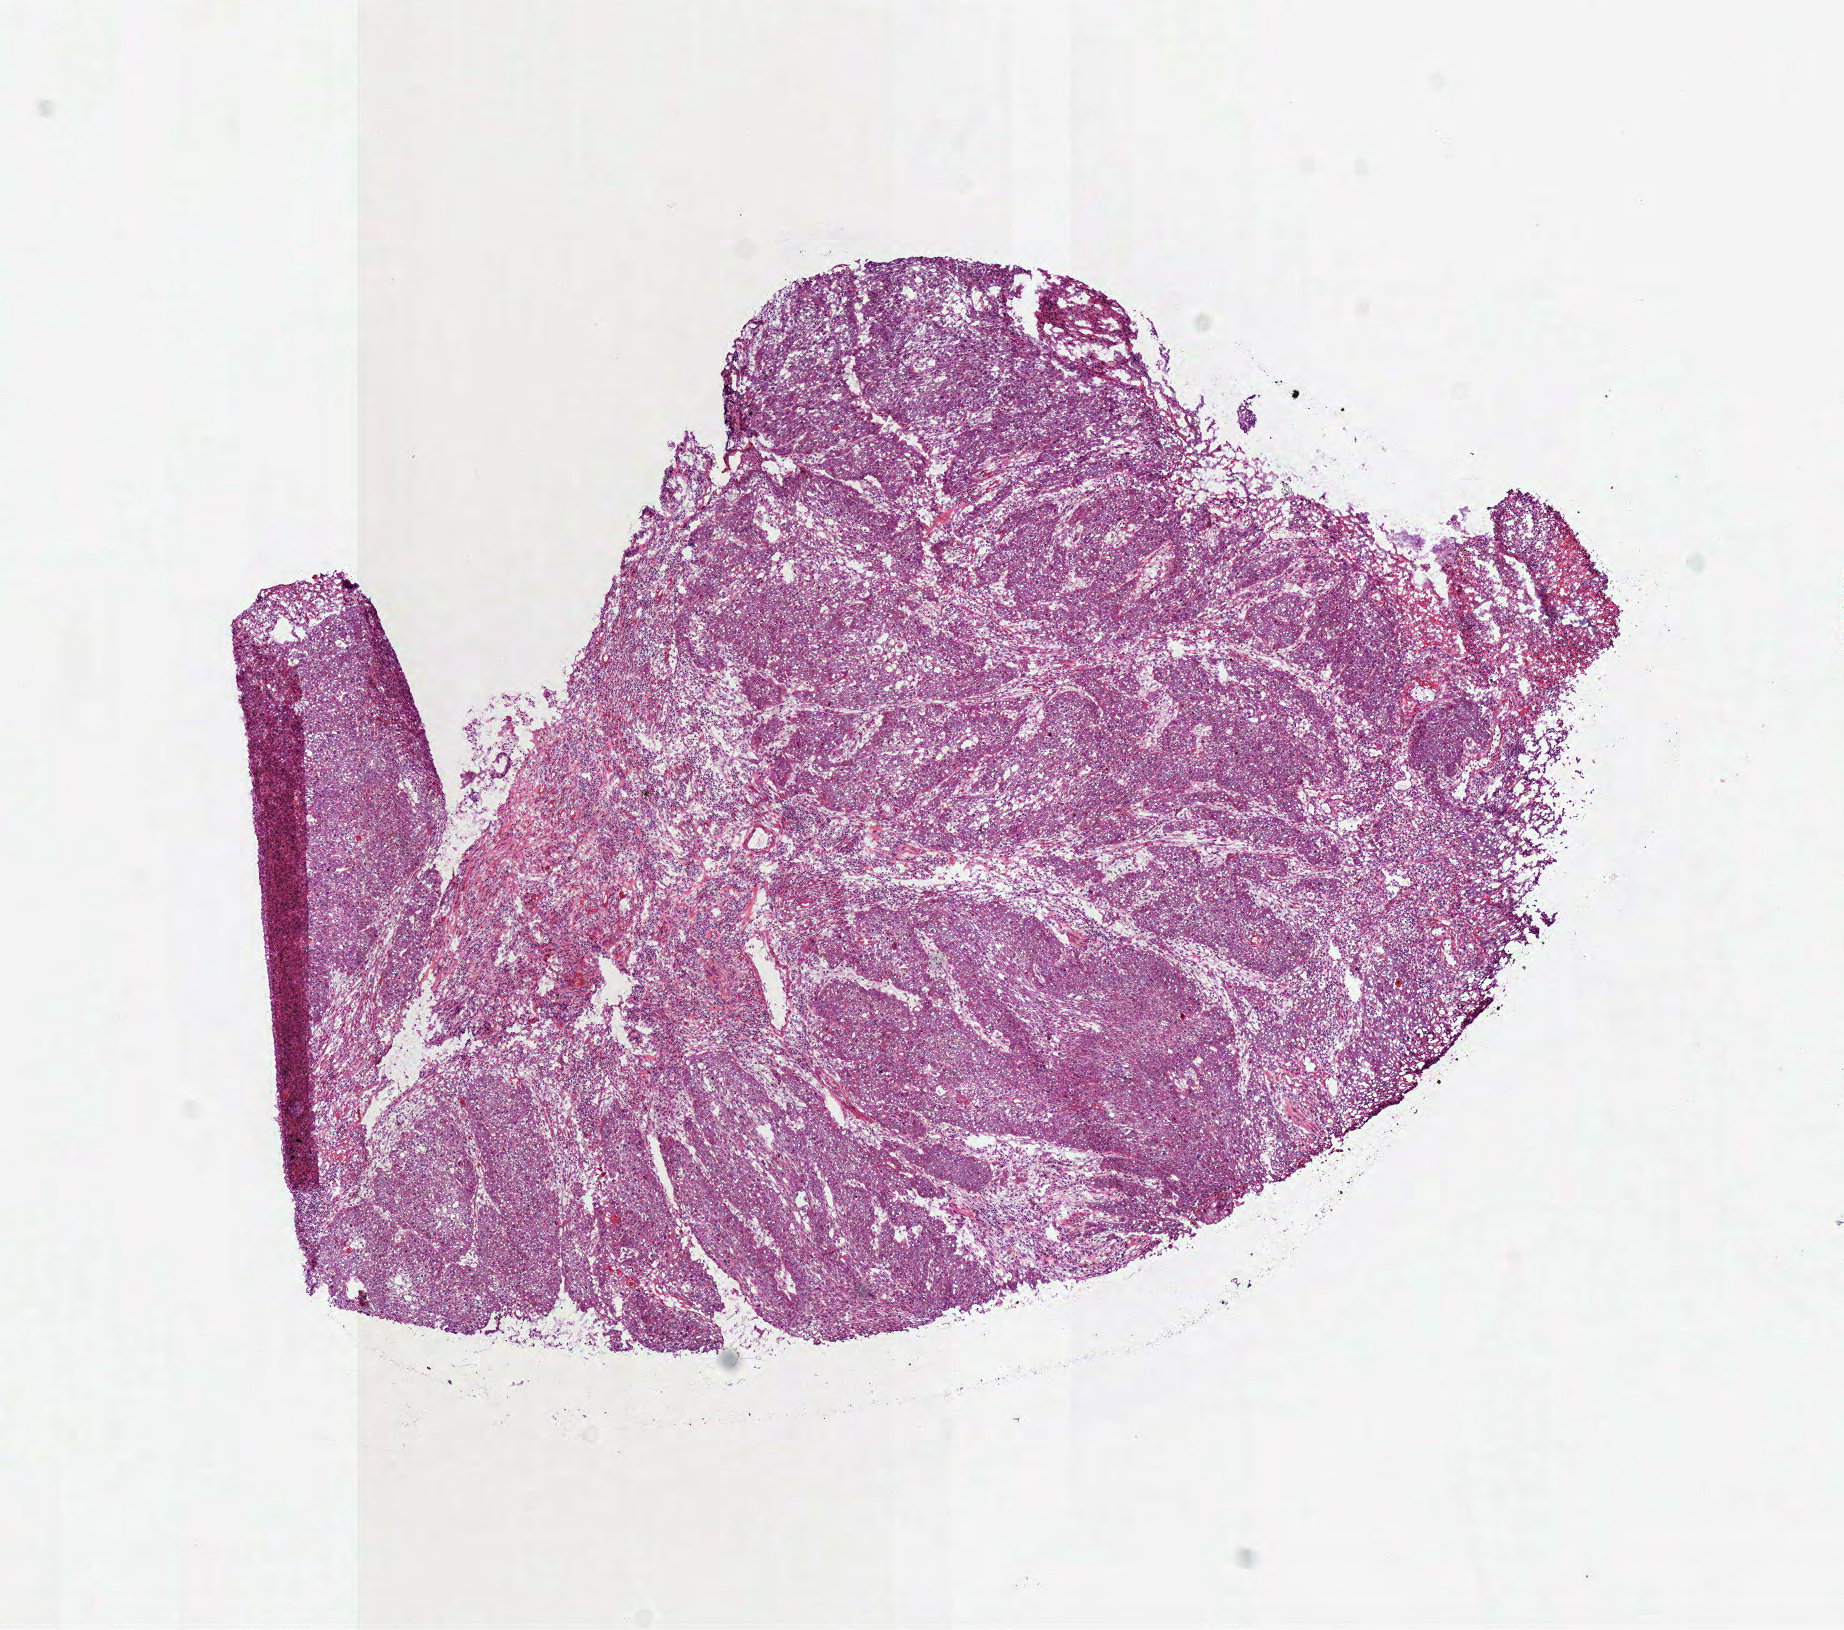
Digitized Hematoxylin and eosin (H&E) stained tissue section (whole slide), whole scanned area (about 7.3 x 6.4 mm, slide scanned at 40x) shown as a low-resolution overview; frozen section from the bottom of the tissue portion; primary tumour sample from the head and neck. Patient: male, age at initial diagnosis 50 years. Histologic grade: G2 (moderately differentiated). Pathologist review of this section (percent, as recorded): tumour cells 90%, tumour nuclei 75%, normal cells 0%, stromal cells 10%, necrosis 0%.
AJCC pathologic stage: II (7th edition). Diagnosis: Squamous cell carcinoma, NOS (tongue, NOS). Laterality: left.